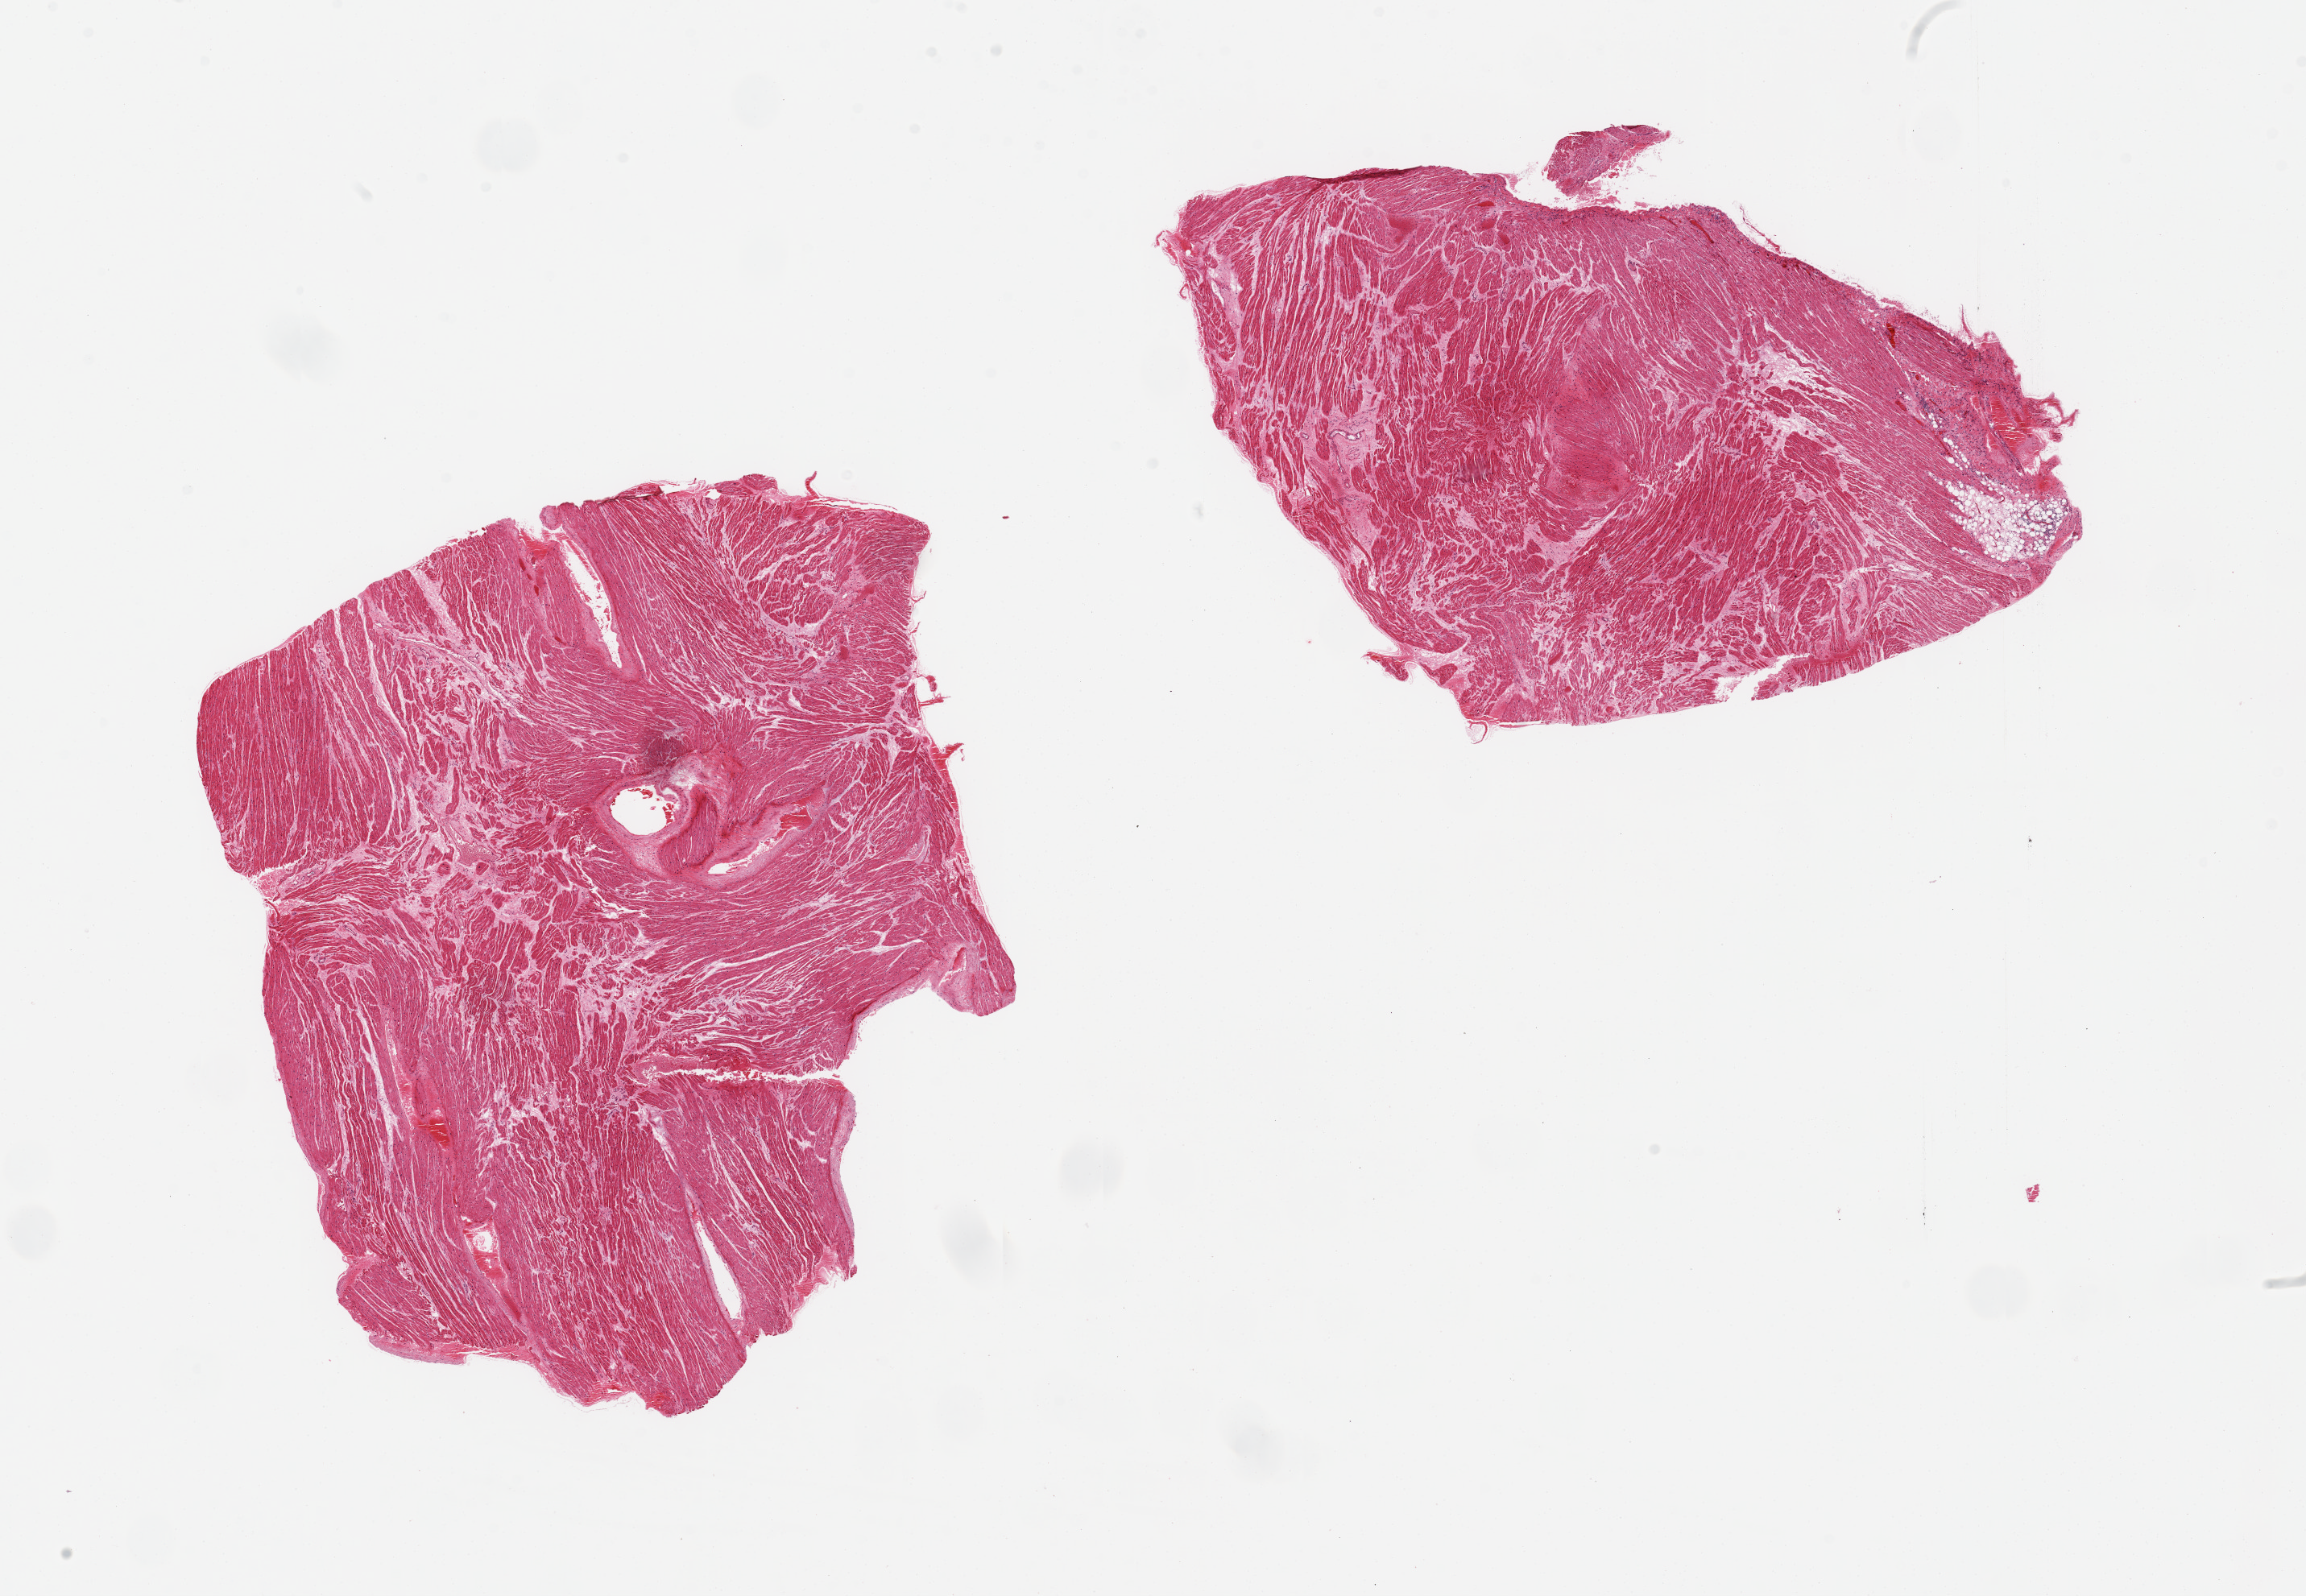
Digitized hematoxylin and eosin (H&E)-stained section, a low-resolution overview of the entire scanned area, about 22.6 x 15.7 mm (from a 20x scan); PAXgene-fixed paraffin-embedded (PFPE) section; sampled site (target tissue): auricular appendage; tissue donor sample. Male donor.
• review note (as recorded): 2 pieces, no abnormalities